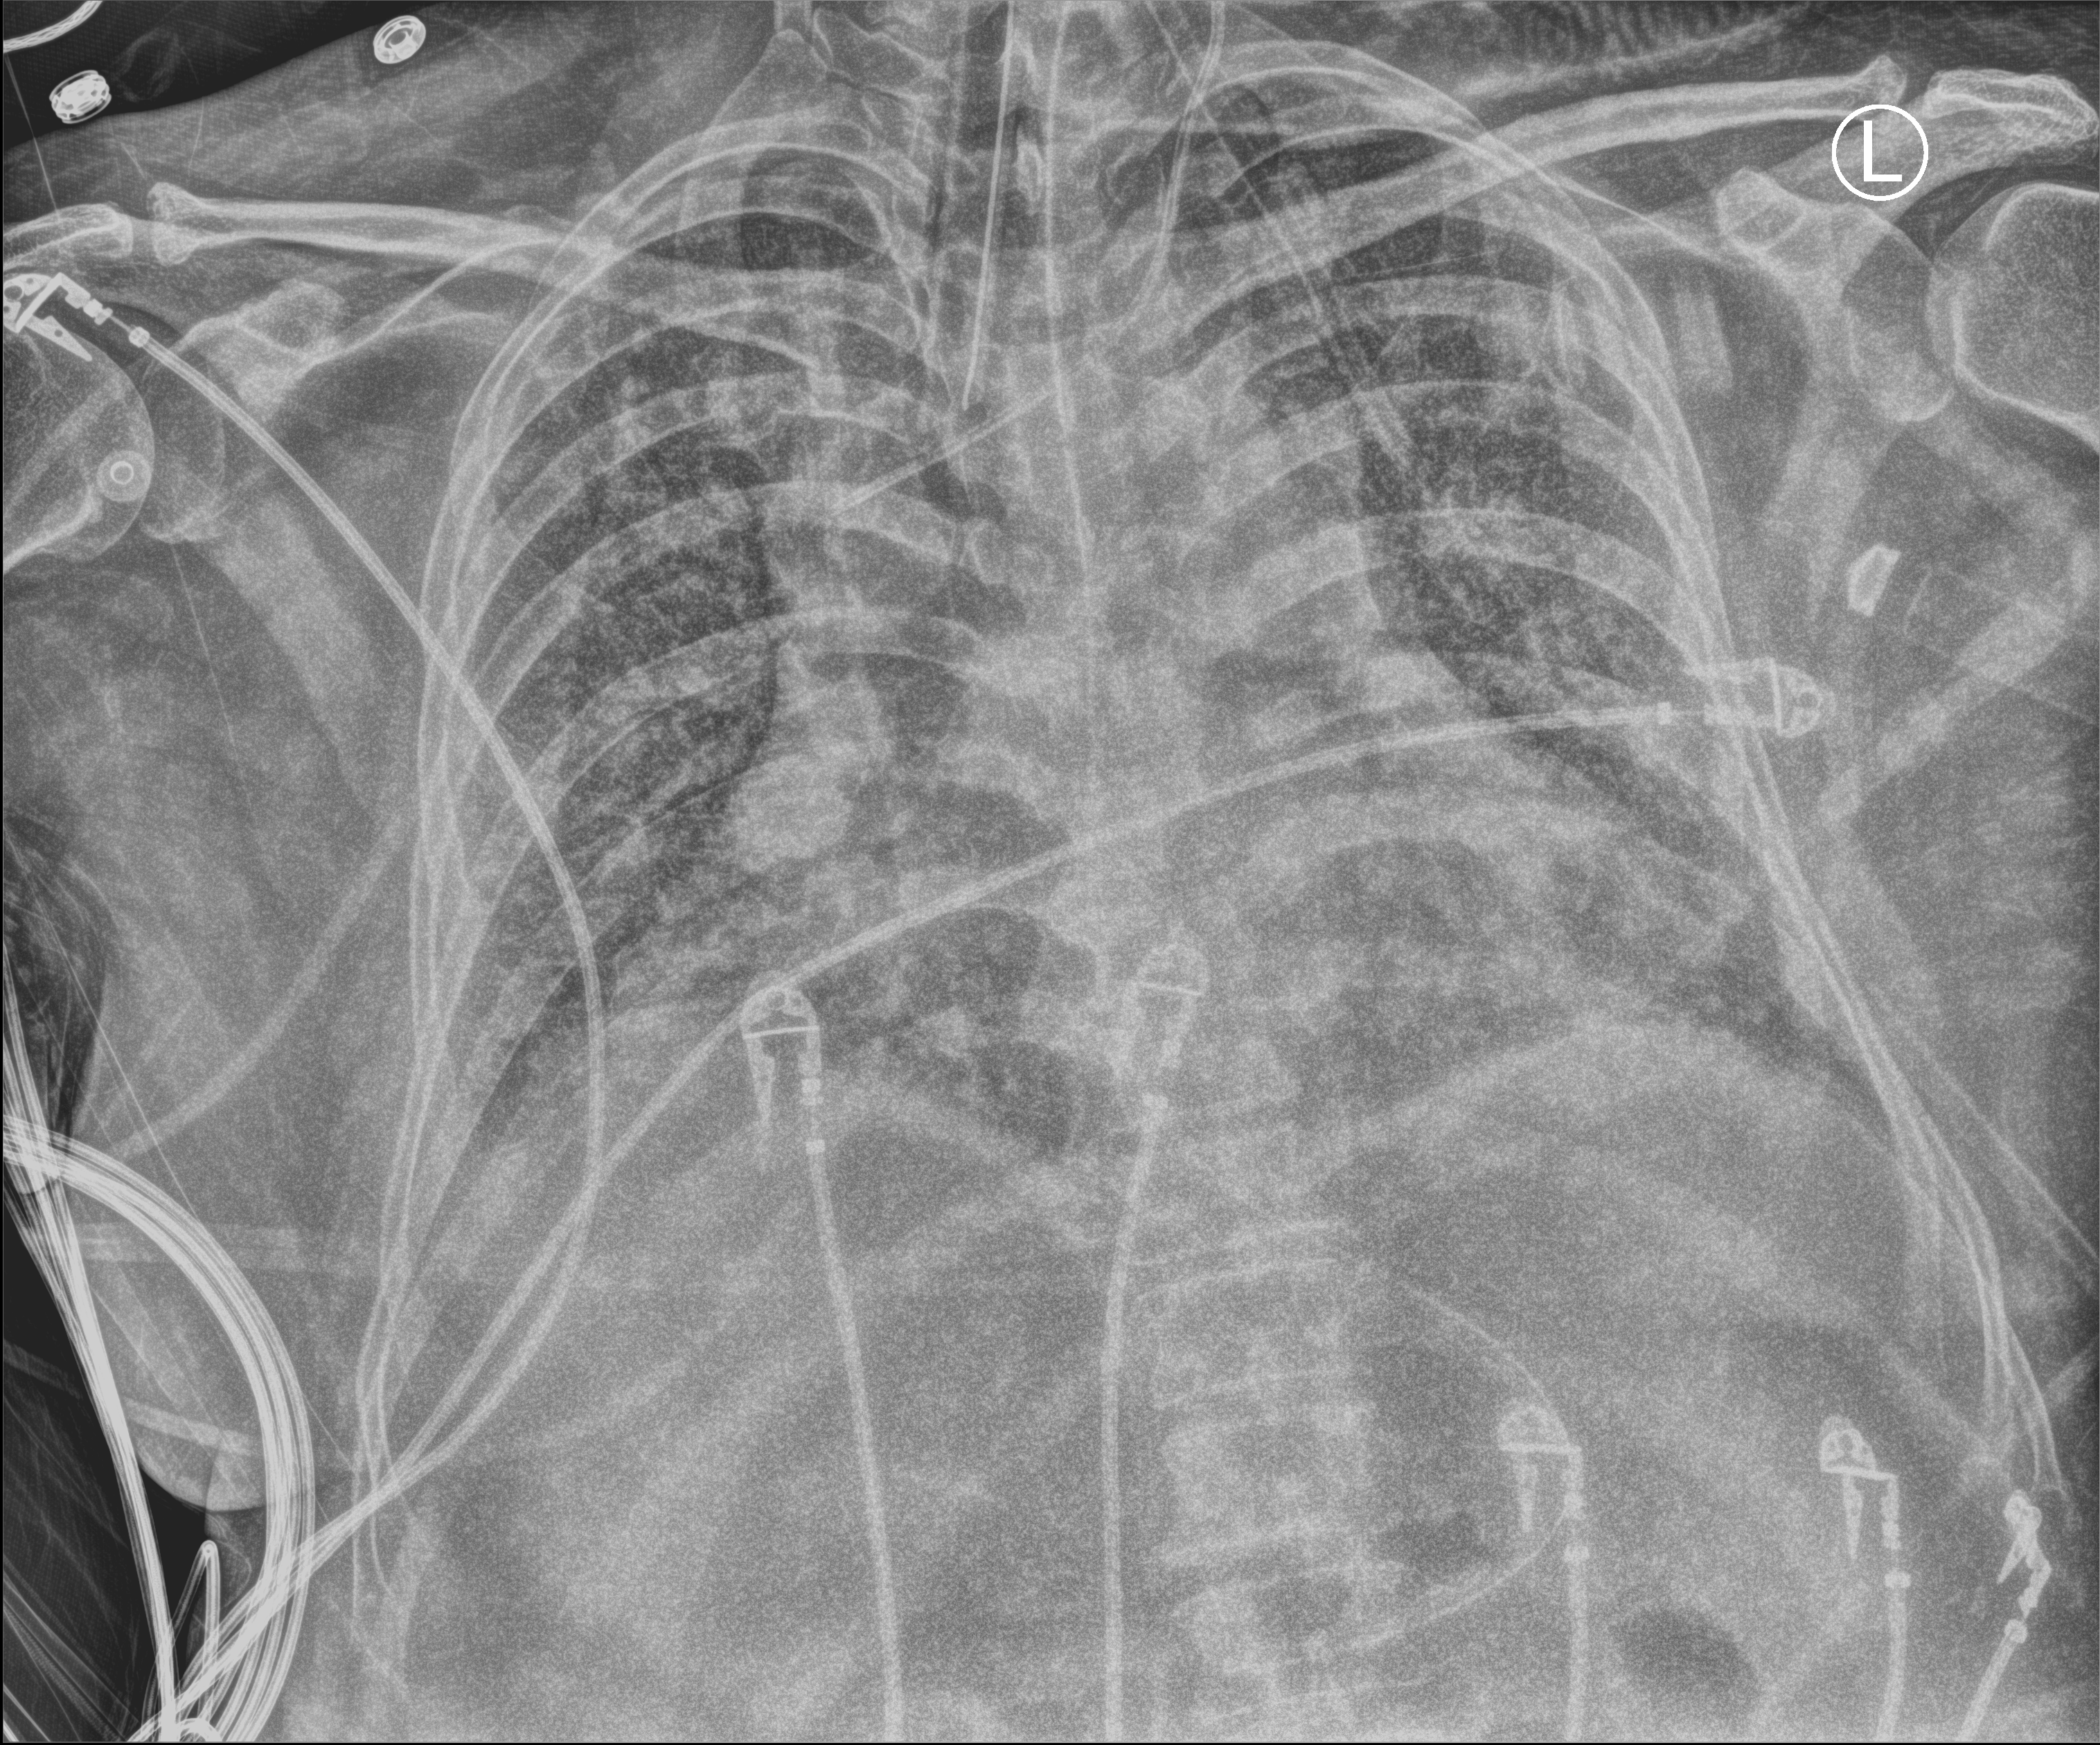
Chest X-ray (portable); anteroposterior (AP) projection. Patient hospitalised with COVID-19, aged 18–59 years.
From the hospital-stay record, not from the radiograph (when in the stay this image was taken is not recorded): COPD (admission record): no.